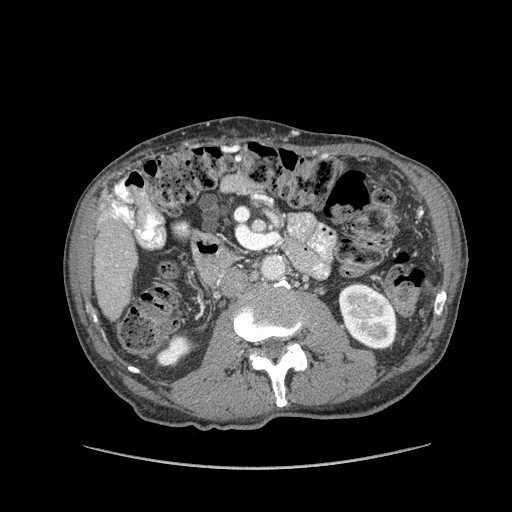
Contrast-enhanced abdominal CT (liver protocol), one axial slice; position 19 of 162 along the scan axis; reconstruction kernel STANDARD; soft-tissue window (W 400 / L 40 HU); 512 × 512 image matrix. Case-level facts recorded for this patient, not image findings: diagnosis: hepatocellular carcinoma (patient treated with transarterial chemoembolisation; whether this scan precedes or follows treatment is not stated here); TNM stage (as recorded): Stage-IIIA; Child-Pugh class: A; tumour size: 9.9 cm.
Outlined on this slice (semi-automatically segmented with operator editing):
- liver parenchyma outside the tumour (the mass and vessels are separate outlines, so this box may not span the whole liver): bounding box <94,198,138,320> (left, top, right, bottom; pixels)
- liver vessels: <111,201,120,219>